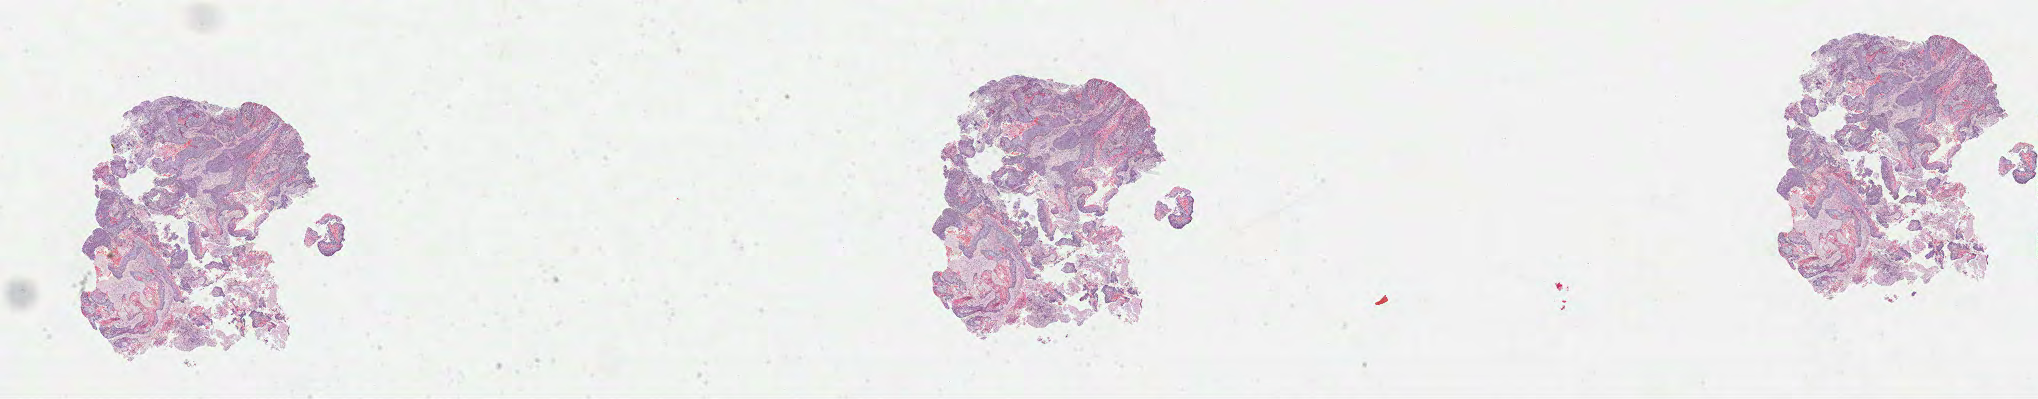
Digitized H&E tissue section (whole slide) — shown as a low-resolution overview of the whole scanned area (about 32.9 x 6.4 mm, from a 40x scan). Formalin-fixed paraffin-embedded (FFPE) diagnostic section. Sample: primary tumour, head and neck. Male patient; age at initial diagnosis 66 years. Histologic grade: G2 (moderately differentiated).
Diagnosis: Squamous cell carcinoma, NOS. AJCC pathologic stage: IVA (7th edition).